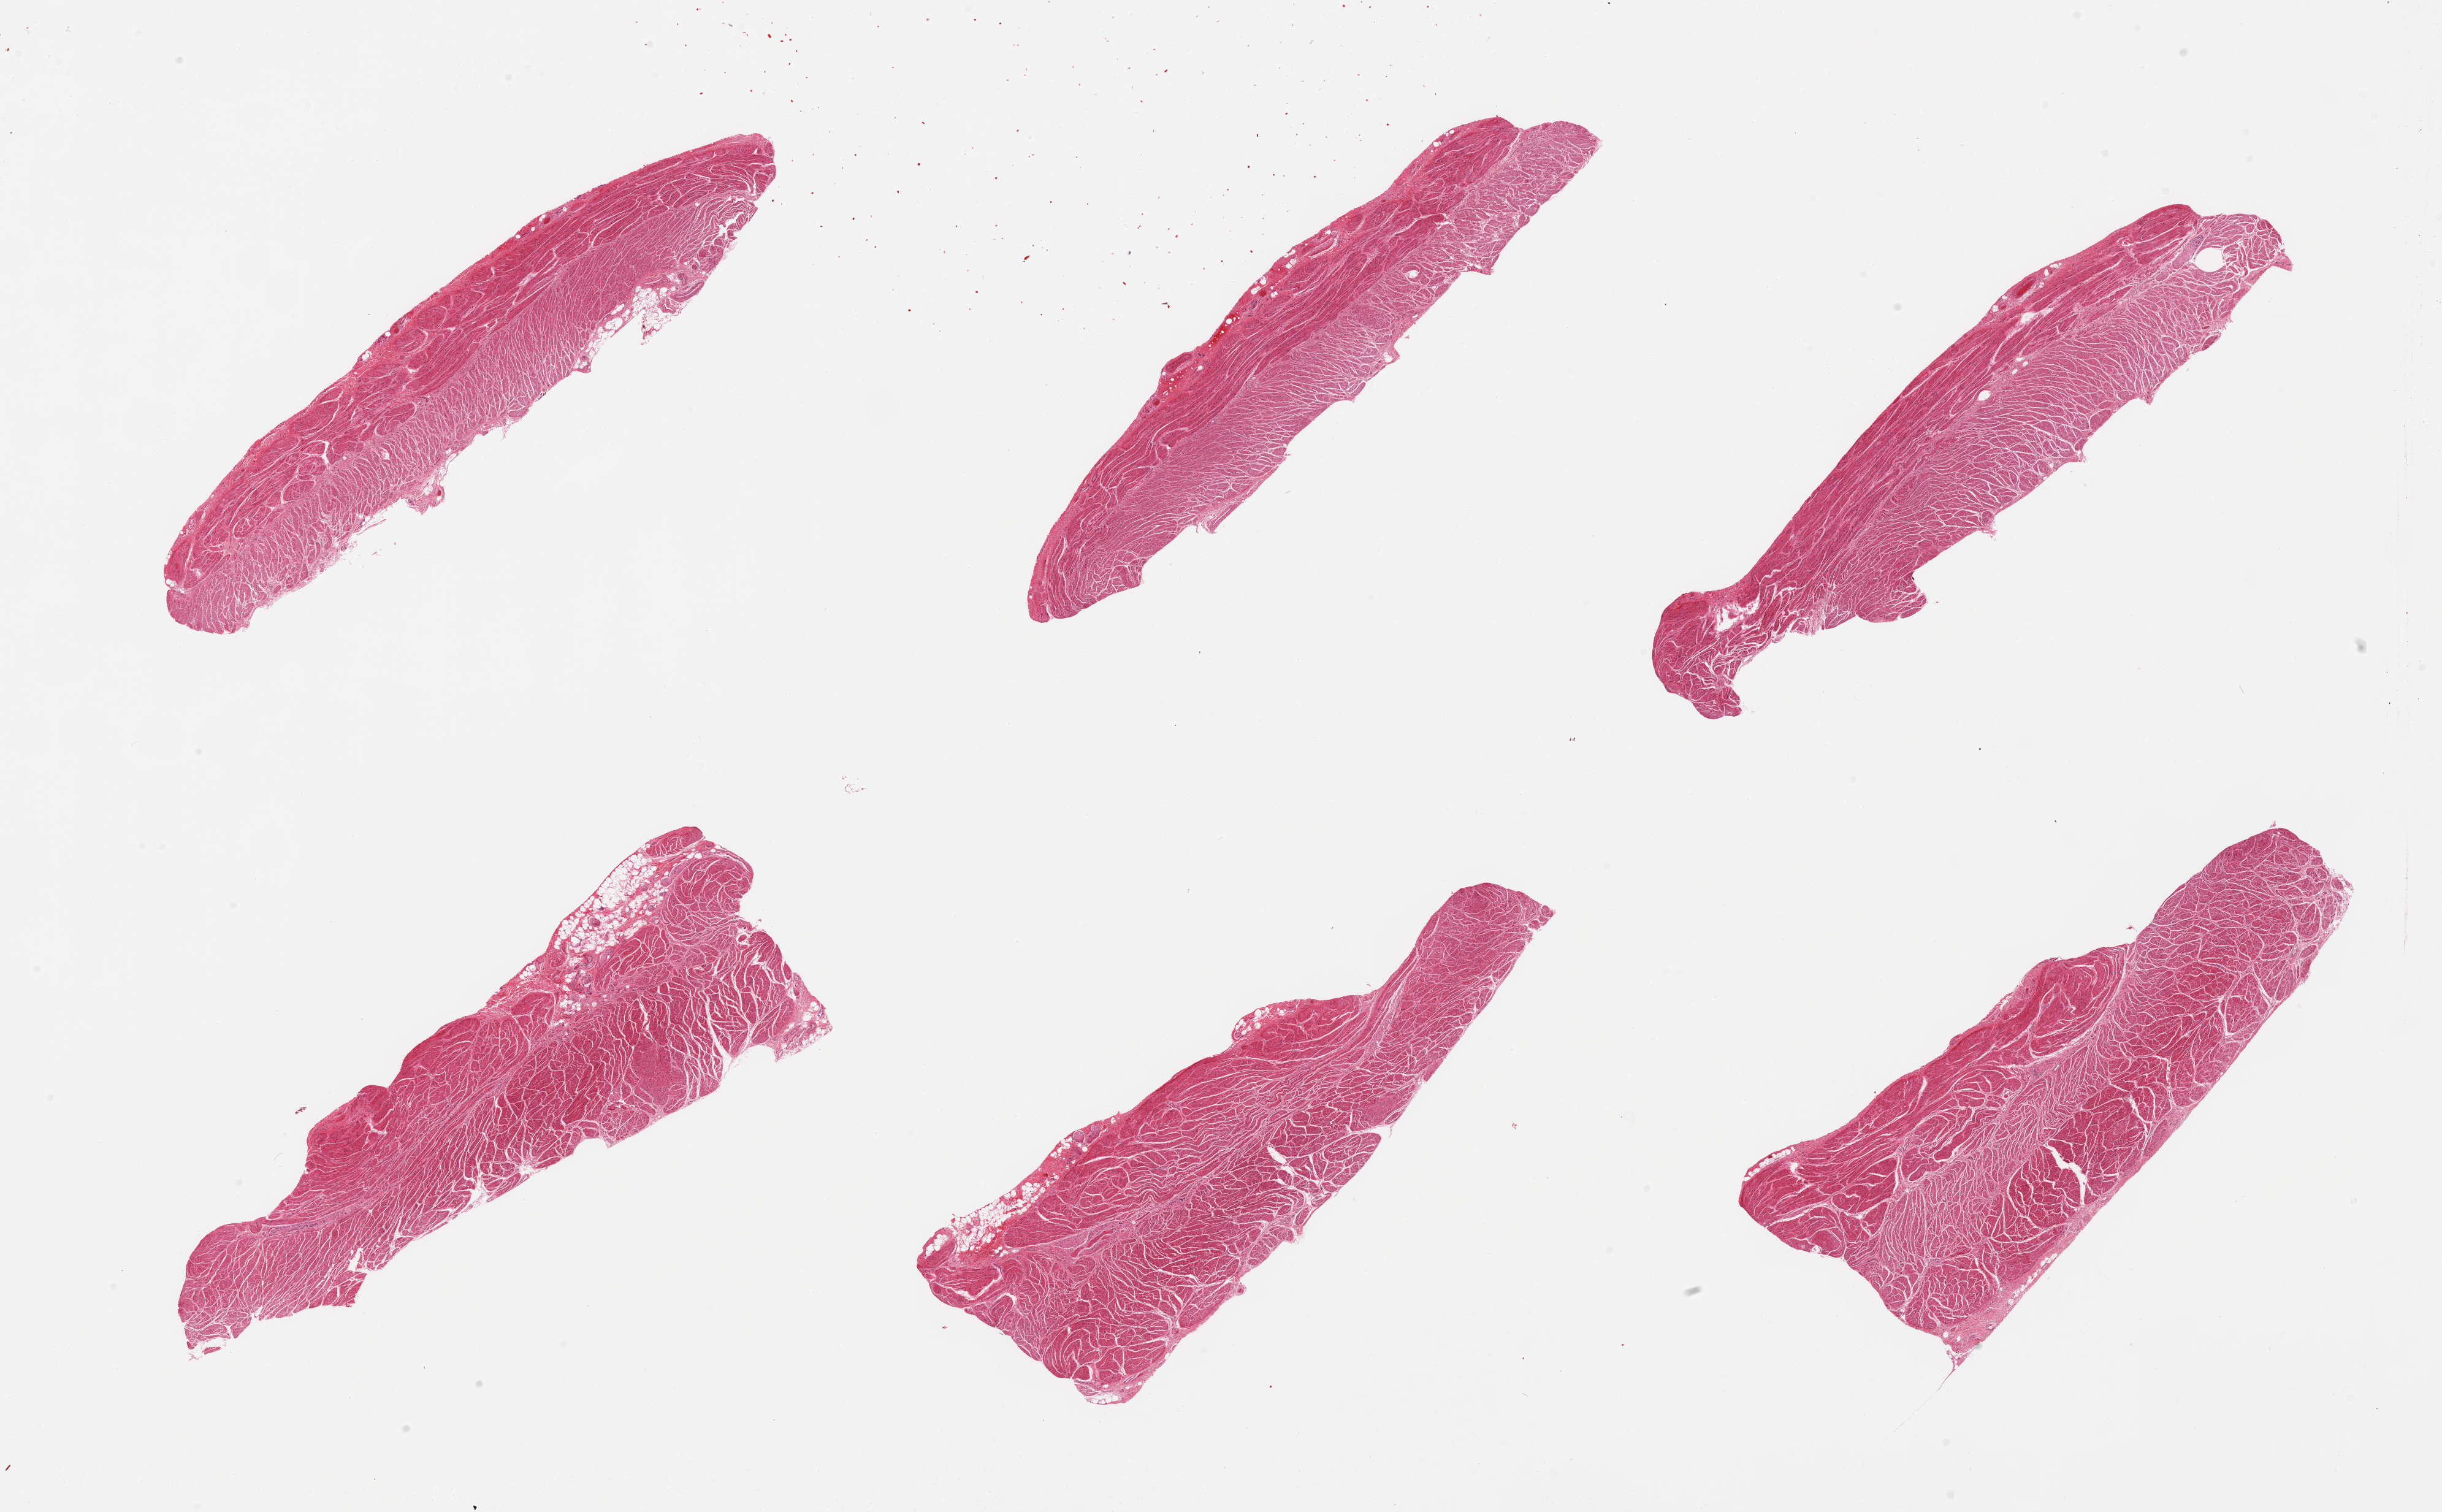
Digitized H&E-stained section — shown as a low-resolution overview of the whole scanned area (about 31.5 x 19.5 mm), PAXgene-fixed paraffin-embedded (PFPE) section, target tissue: gastroesophageal junction, tissue donor sample. Donor: female.
Review note (as recorded): 6 pieces, well trimmed.